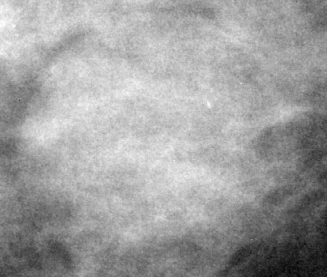
Crop from a digitized film mammogram around one marked abnormality; right breast; CC view; BI-RADS breast density category 3 (scale 1–4).
Finding: mass, shape round, margins circumscribed; BI-RADS assessment category 3; subtlety rating 4 on a 1 (subtle) to 5 (obvious) scale; pathology (as recorded): benign.